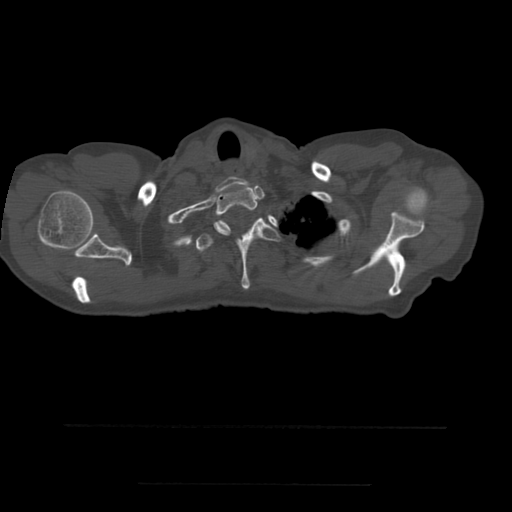
CT including the spine, one axial slice. Position 441 of 544 along the scan axis. Bone window (W 1800 / L 400 HU). 1.25 mm slice thickness. 512 × 512 image matrix. Patient age 58 years. Case-level facts recorded for this patient, not image findings: primary cancer: lung.
Outlined on this slice (semi-automatically segmented with operator editing):
- T1 vertebra: bounding box (x1, y1, x2, y2) in pixels: (214, 184, 258, 235)
- T2 vertebra: (196, 218, 281, 290)